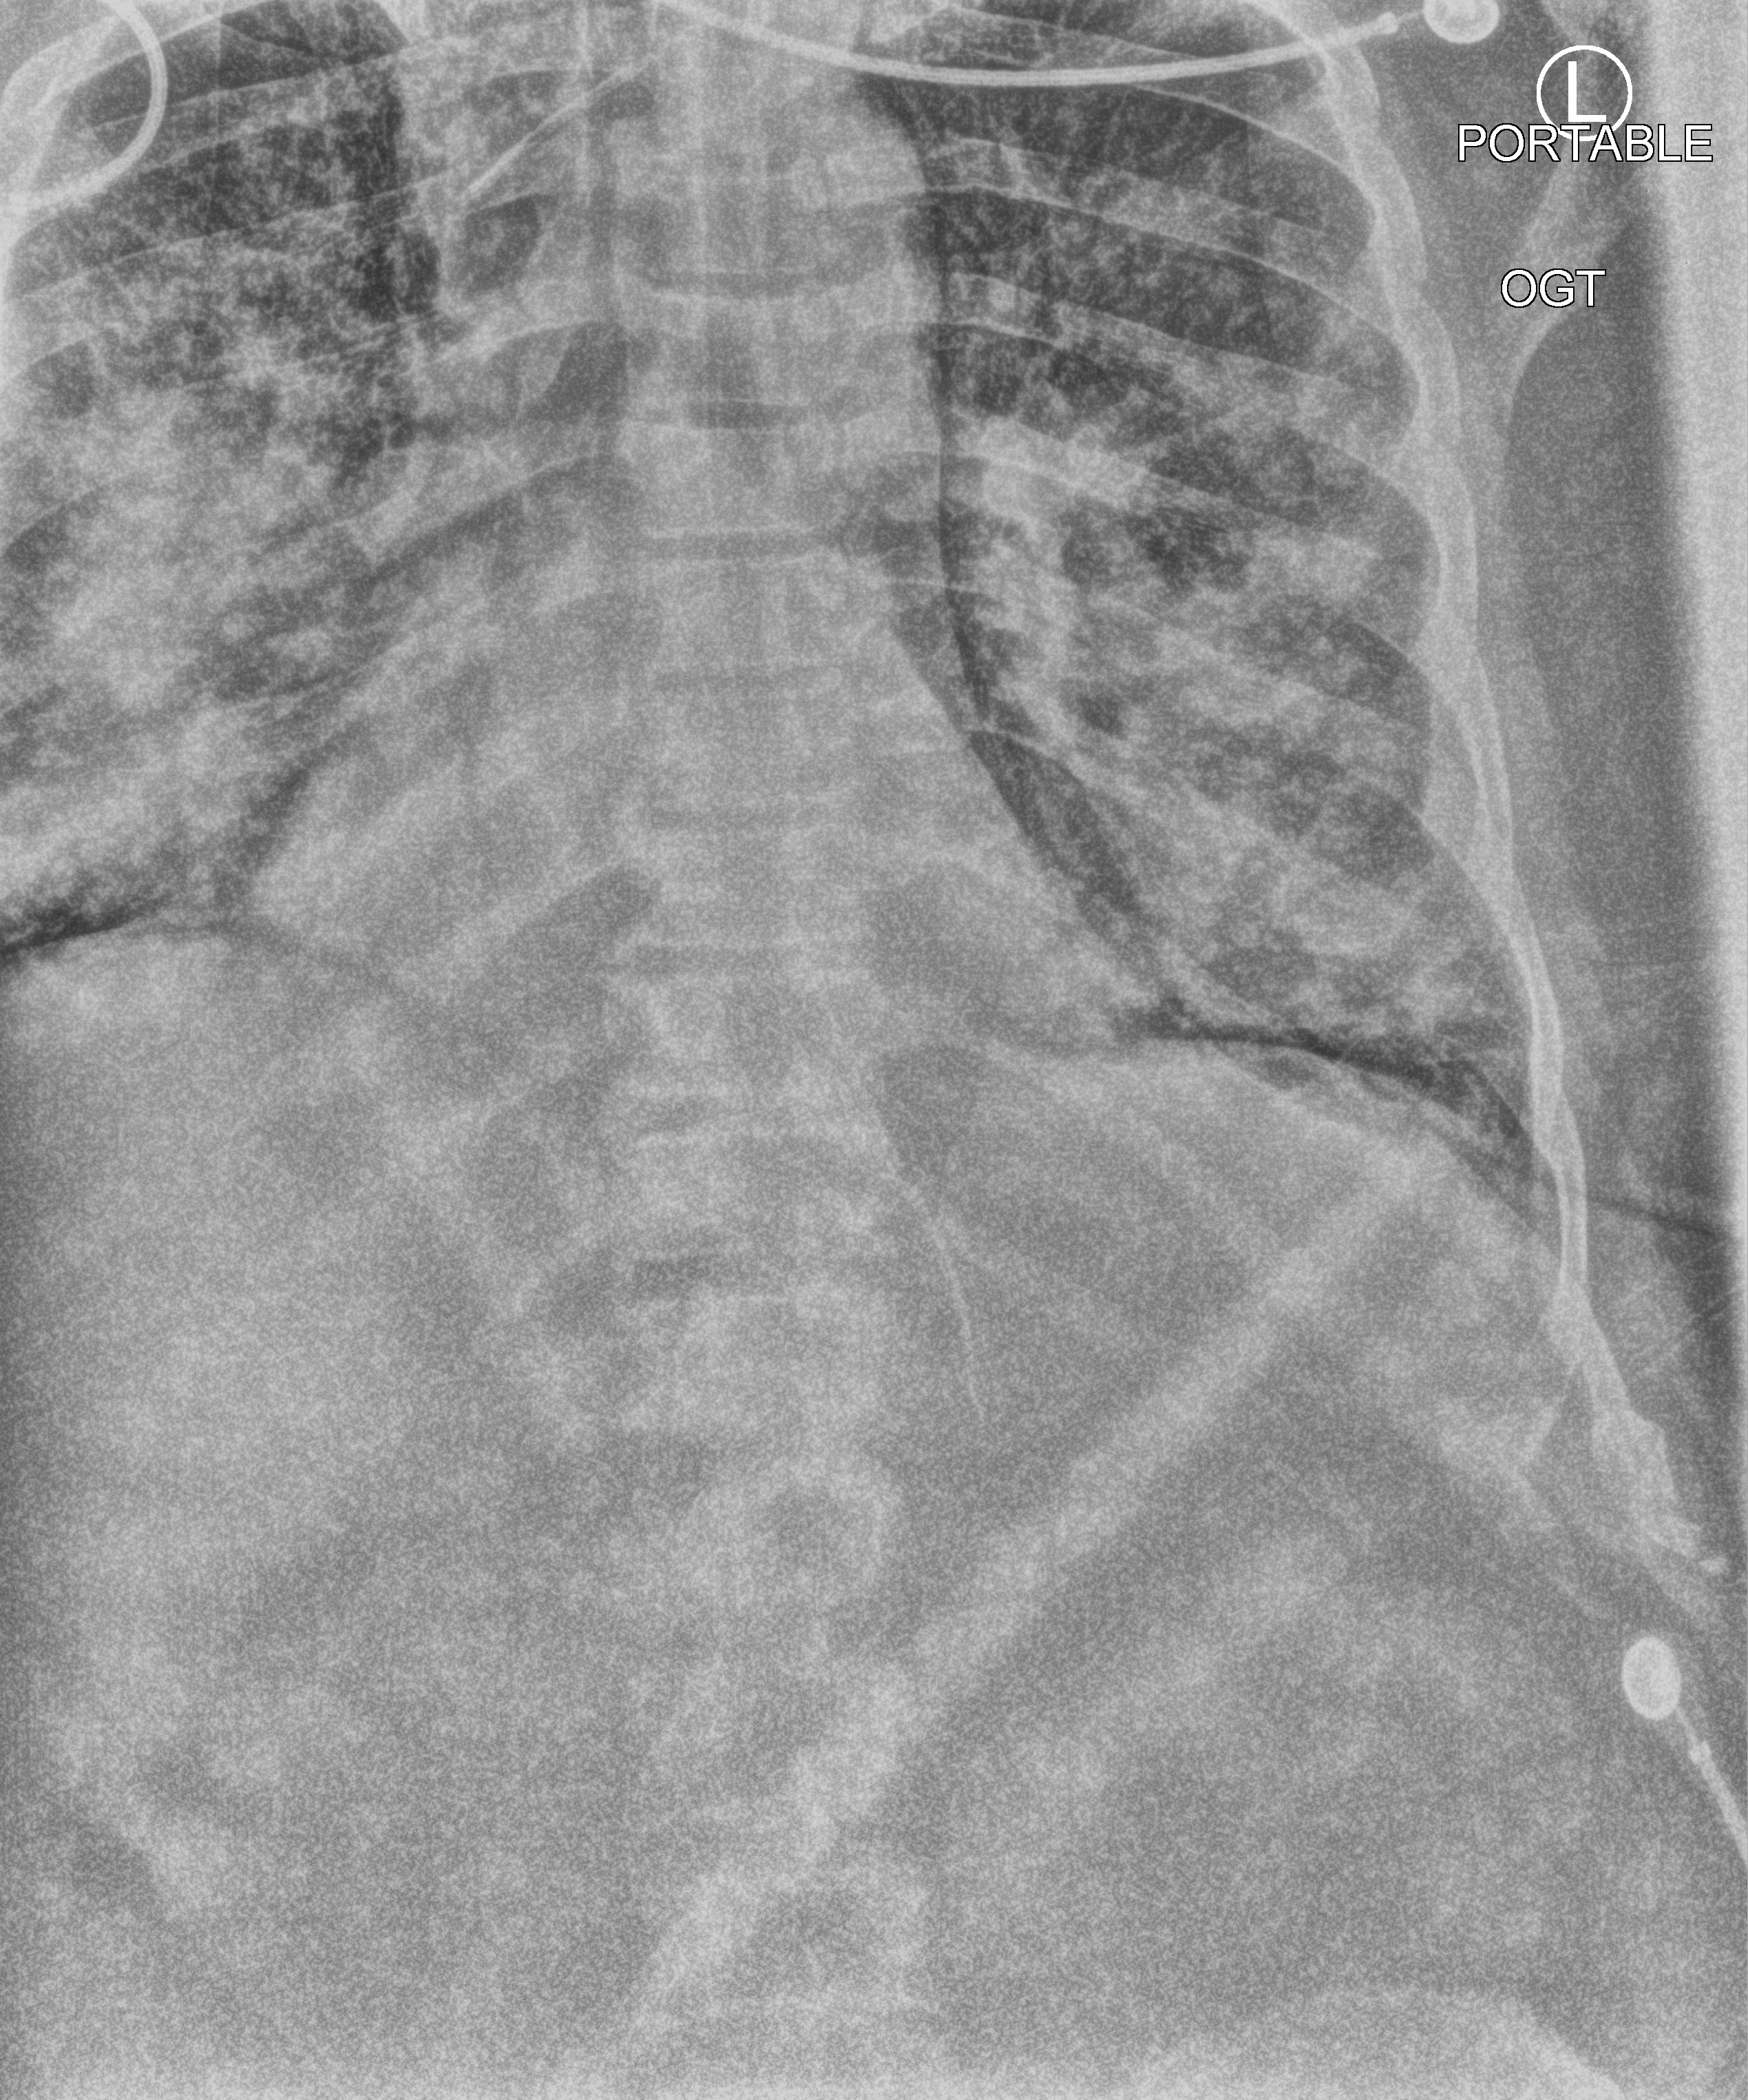
Chest X-ray (portable), anteroposterior (AP) projection. Adult patient hospitalised with COVID-19, age 18–59 years.
Hospital-stay facts (about this admission, not read from this image; timing relative to this image not recorded):
- admitted to intensive care during this hospital stay: yes
- mechanically ventilated during this hospital stay: yes
- hypertension (admission record): yes